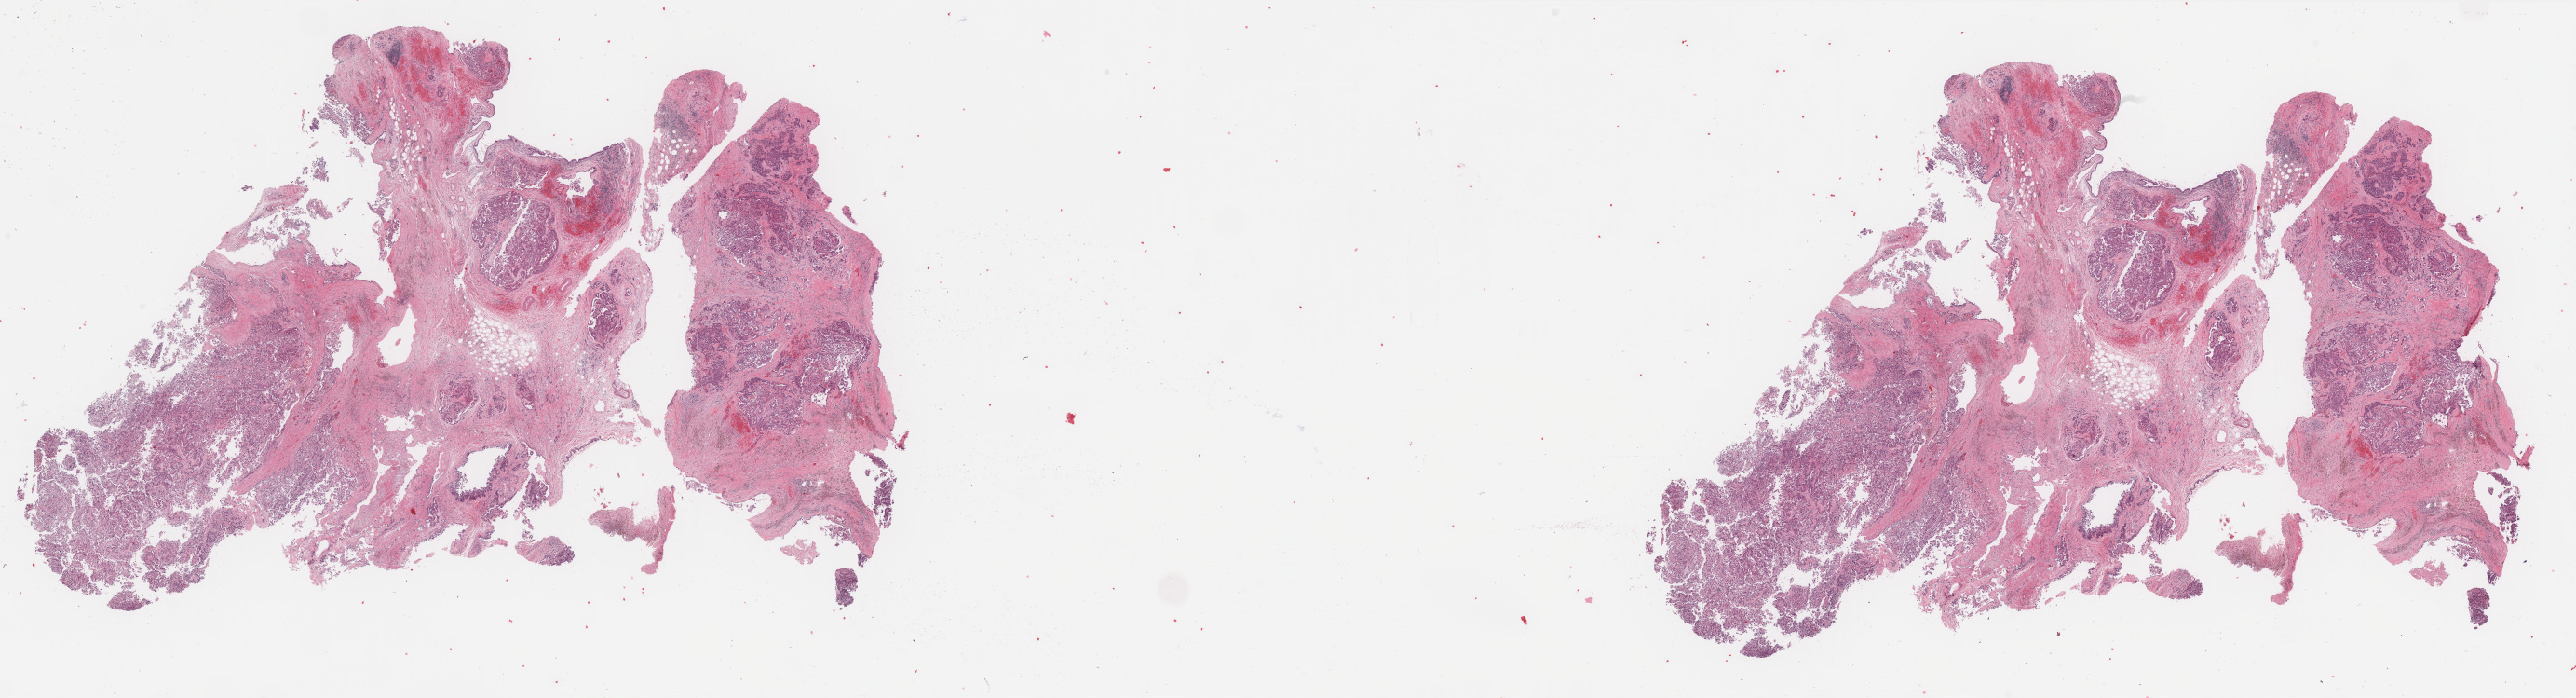
Hematoxylin and eosin (H&E) stained whole-slide image, shown as a low-resolution overview of the whole scanned area (about 43.8 x 11.9 mm, from a 40x scan), formalin-fixed paraffin-embedded (FFPE) diagnostic section, kidney, primary tumour sample. Male patient; age at initial diagnosis 70 years.
AJCC pathologic stage: III (7th edition). Laterality: left. Histologic diagnosis: Papillary adenocarcinoma, NOS.